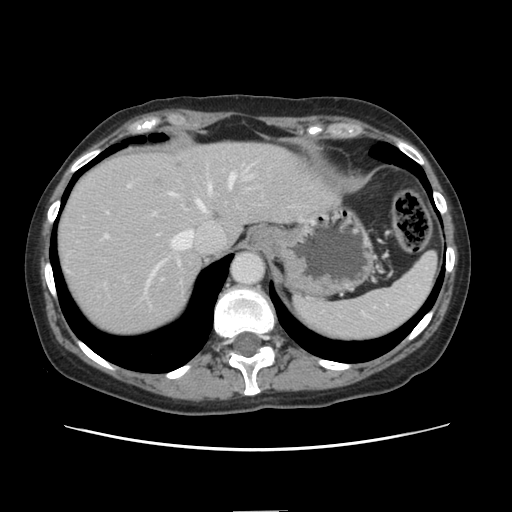
Contrast-enhanced abdominal CT, one axial slice. Slice 114 of 141 in the series (ordered by position). Intravenous contrast given. Soft-tissue window (W 400 / L 40 HU). 2.5 mm slice thickness. 512 × 512 image matrix. Female patient, age 63 years. Case-level facts recorded for this patient, not image findings: diagnosis: colorectal cancer liver metastases, imaged before liver resection; multiple liver metastases: yes; largest metastasis: 3.2 cm.
Outlined on this slice (outlined manually by an expert reader):
- hepatic veins: bounding box <147,174,235,286> (left, top, right, bottom; pixels)
- liver: <58,142,334,337>
- planned liver remnant (the part of the liver to remain after resection): <196,143,332,240>
- portal vein (with intrahepatic branches): <233,167,250,177>
- liver metastasis: <153,177,162,186>